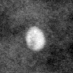
Region of interest cut from a scanned film mammogram (one marked finding); left breast; CC view; BI-RADS breast density category 2 (scale 1–4).
- Calcifications, morphology coarse / round and regular / lucent center; BI-RADS assessment category 2; benign; no additional work-up was recommended (benign without callback).